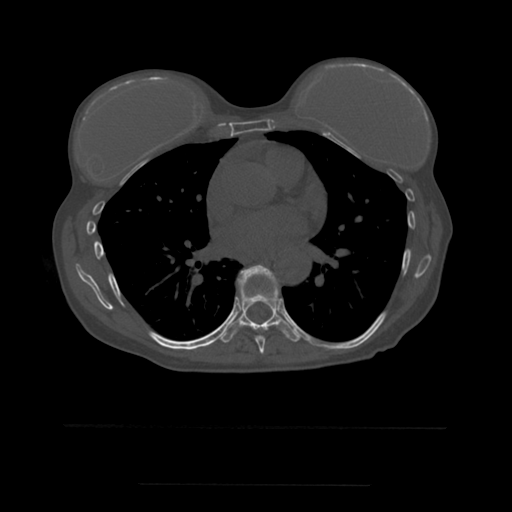
CT including the spine, one axial slice. Position 347 of 544 along the scan axis. Bone window (W 1800 / L 400 HU). 1.25 mm slice thickness. 512 × 512 image matrix. Patient age 58 years. From the clinical record (not read from this slice): primary cancer: lung.
Annotated regions visible in this slice (semi-automatic segmentation, software-assisted and operator-edited):
- T7 vertebra: box from (x=238, y=265) to (x=279, y=354) px
- T8 vertebra: (x=221, y=274)–(x=300, y=343)